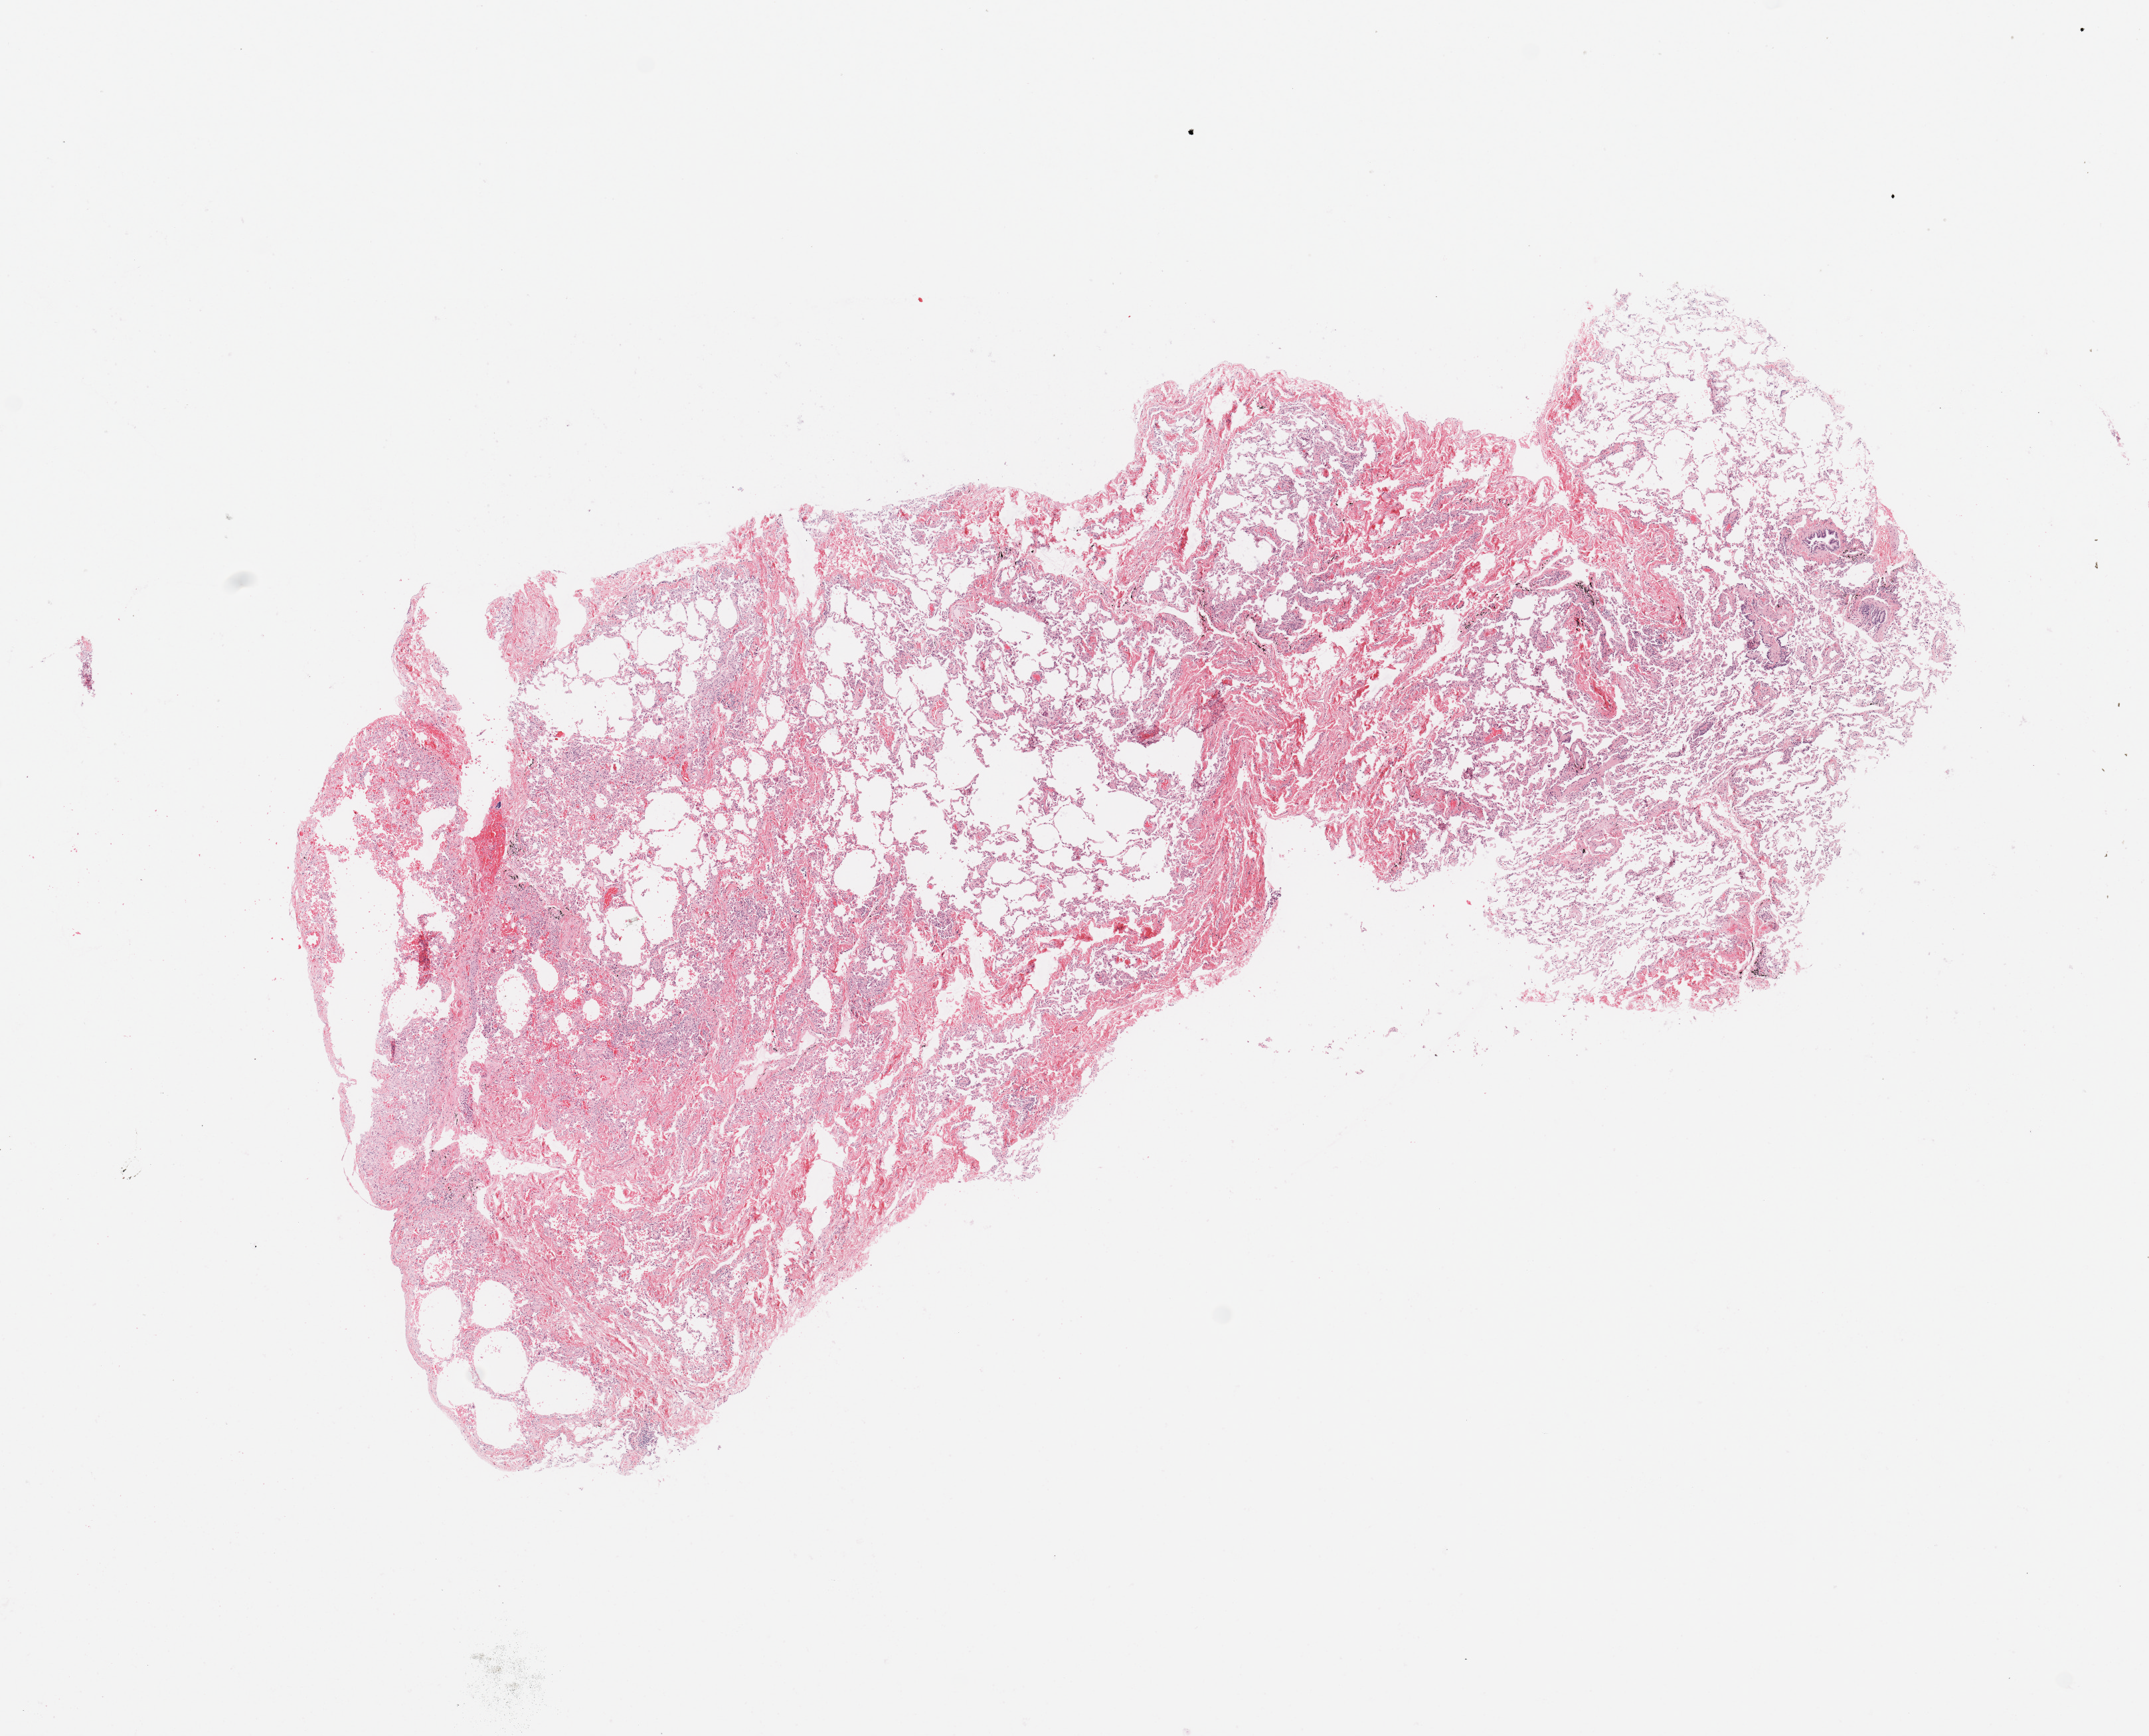
Digitized Hematoxylin and eosin (H&E) stained tissue section (whole slide) — low-resolution overview of the scanned area, about 12.8 x 10.3 mm (acquisition: 20x scan), normal (non-tumour) tissue sample, sampled site: lung. Male, 58 y/o.
This section: normal (non-tumour) tissue from the same patient. Patient diagnosis: Adenocarcinoma, NOS.